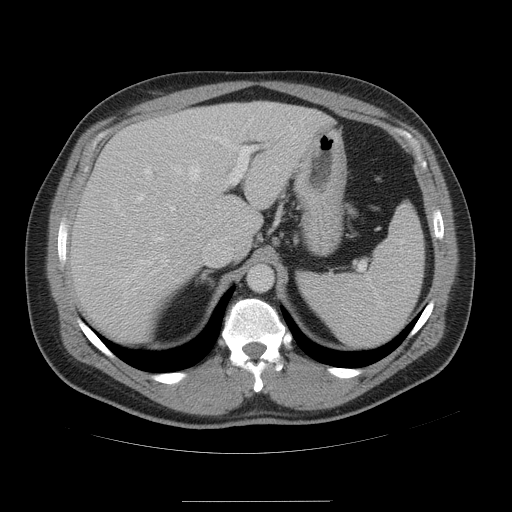
Contrast-enhanced abdominal CT, one axial slice. Position 36 of 54 along the scan axis. 120 kVp. Intravenous contrast given. Soft-tissue window (W 400 / L 40 HU). 512 × 512 image matrix. Male patient, age 40 years. From the clinical record (not read from this slice): diagnosis: colorectal cancer liver metastases, imaged before liver resection; multiple liver metastases: no; largest metastasis: 15 cm; chemotherapy before resection: no.
Structures marked on this image (manually delineated by an expert):
- hepatic veins: bounding box (x1, y1, x2, y2) in pixels: (119, 160, 201, 286)
- liver: (70, 101, 333, 344)
- planned liver remnant (the part of the liver to remain after resection): (185, 101, 333, 269)
- portal vein (with intrahepatic branches): (138, 134, 254, 212)